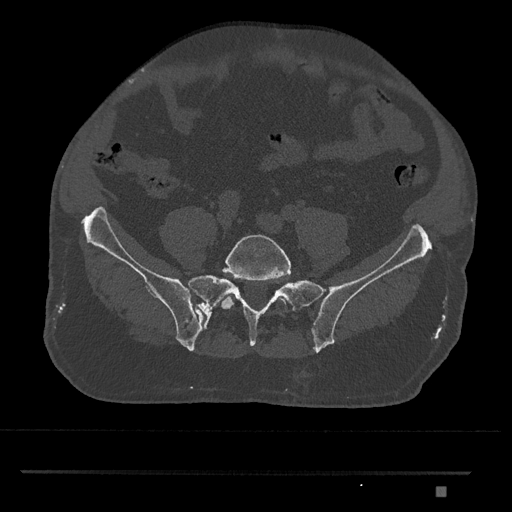
CT including the spine, one axial slice; slice 528 of 1134 in the series (ordered by position); 120 kVp; bone window (W 1800 / L 400 HU); 0.5 mm slice thickness; 512 × 512 image matrix, field of view 429 × 429 mm. Male patient, age 65 years. From the clinical record (not read from this slice): primary cancer: prostate.
Annotated regions visible in this slice (semi-automatic segmentation, software-assisted and operator-edited):
- L5 vertebra: bounding box <221,234,291,311> (left, top, right, bottom; pixels)